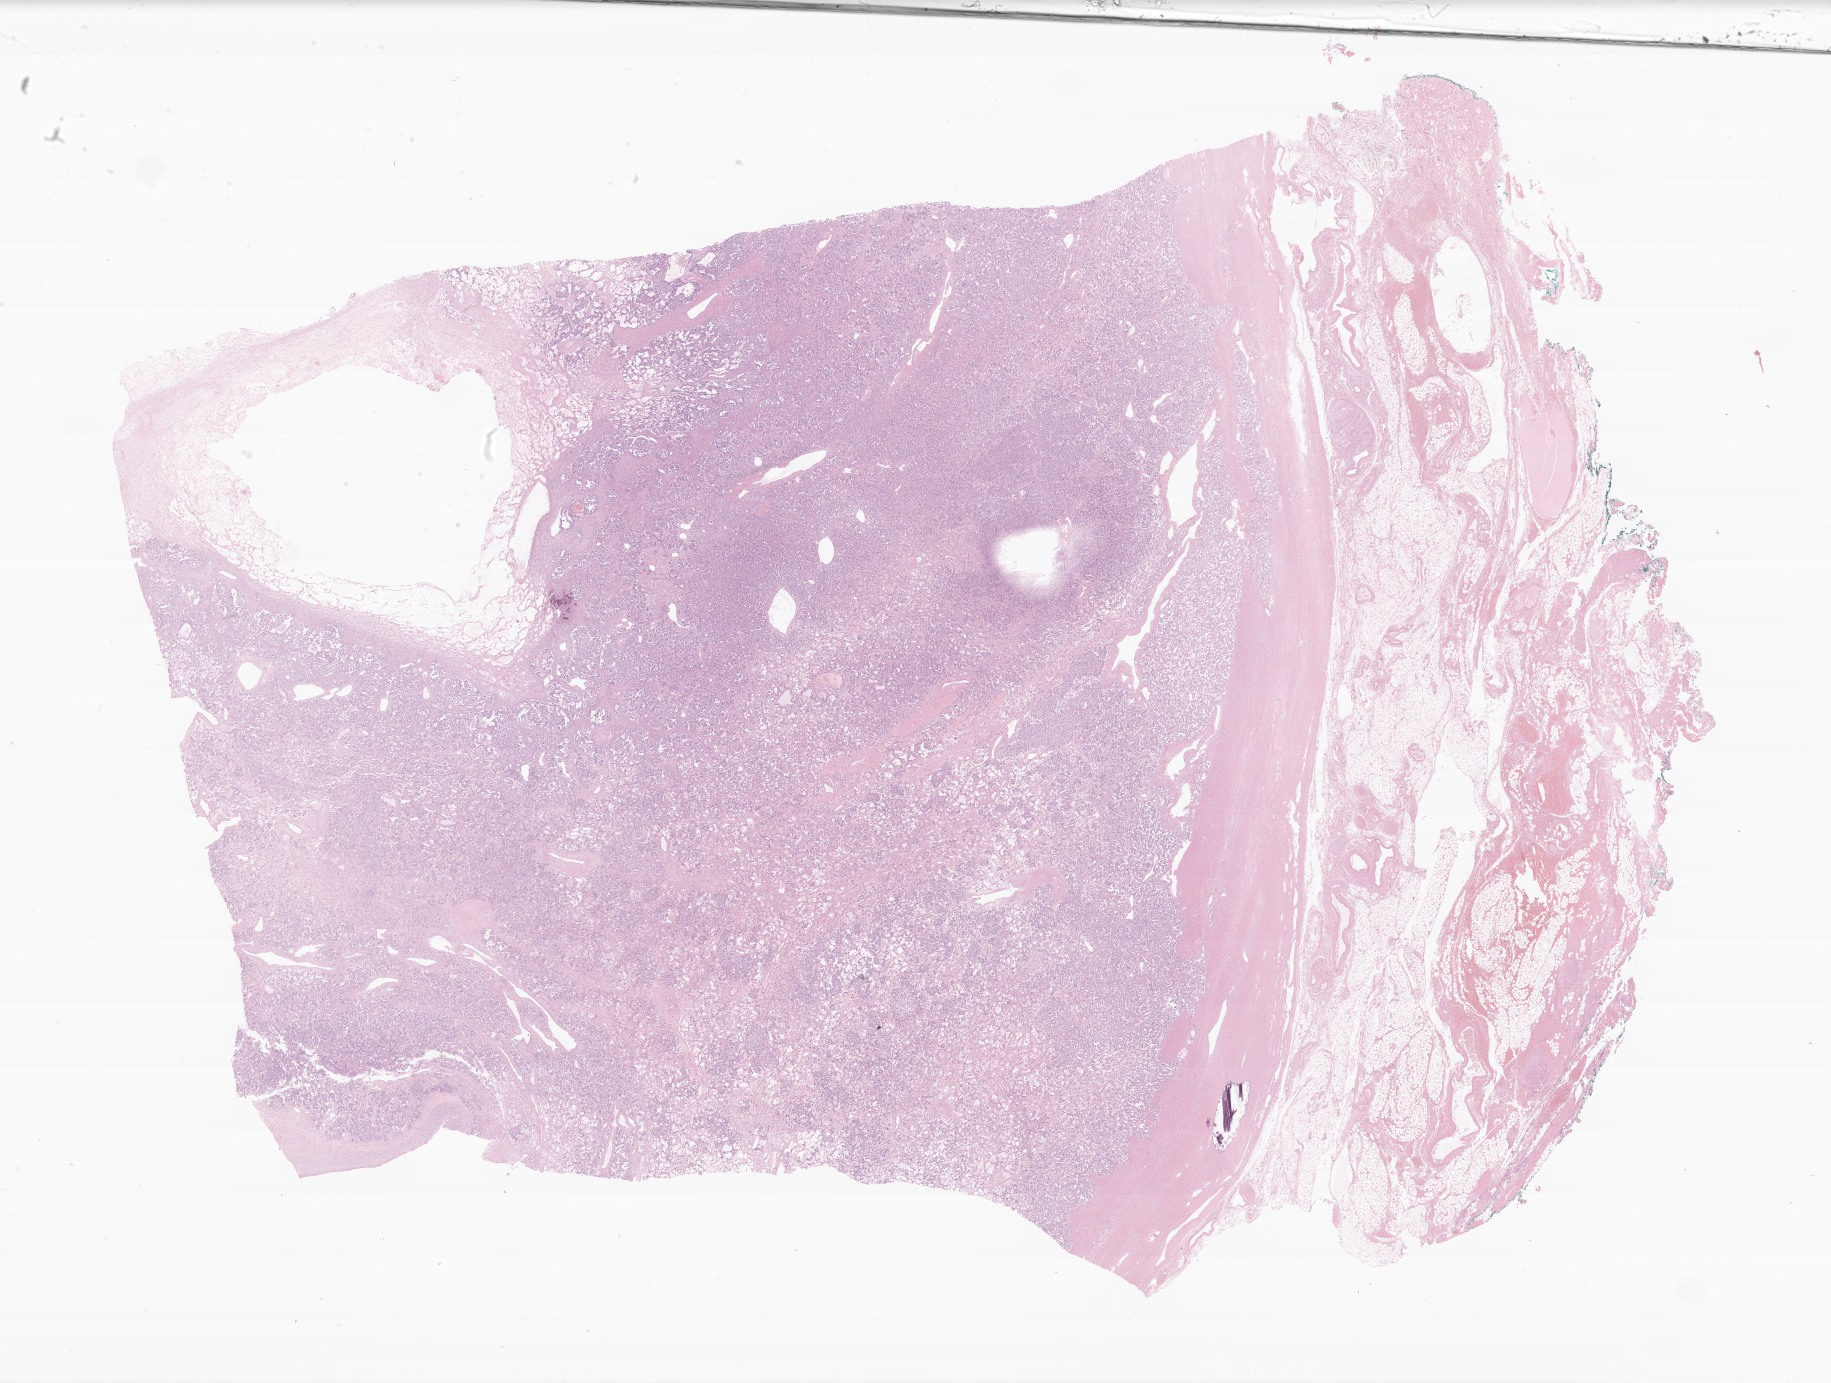
Digitized hematoxylin and eosin (H&E)-stained section of tumor tissue from the adrenal gland, shown as a low-resolution overview of the whole scanned area (about 30.8 x 23.3 mm). Formalin-fixed, paraffin-embedded (FFPE) tissue. Patient female; age 186 months.
Diagnosis: Adrenal cortical carcinoma.